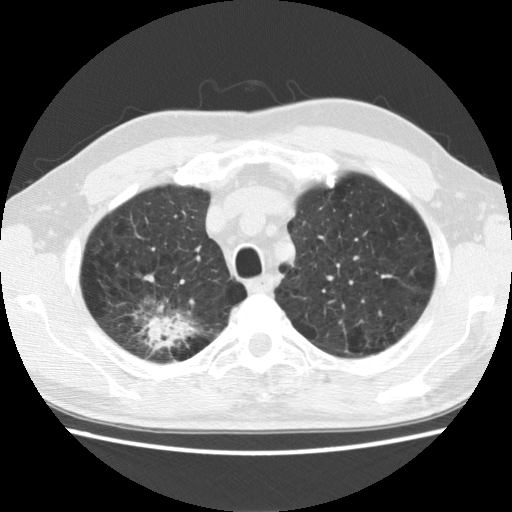
Low-dose screening chest CT, one axial slice. Position 110 of 142 along the scan axis. 120 kVp. Lung window (W 1500 / L -600 HU). 2.5 mm slice thickness. 512 × 512 image matrix, field of view 340 × 340 mm.
Outlined on this slice (outlined manually by an expert reader):
- lesion 1 (tumor, upper lobe of right lung): box from (x=148, y=319) to (x=176, y=346) px